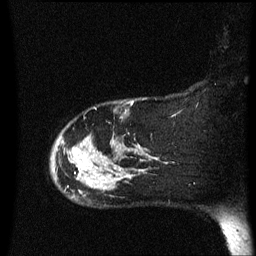
Breast MRI (dynamic contrast-enhanced), one sagittal slice. Dynamic contrast-enhanced series, image 2 of 3 at this slice position (ordered by acquisition). 1.5 T. TE 4.2 ms, TR 8.4 ms. 256 × 256 image matrix, field of view 200 × 200 mm. Female patient, age 47 years.
Structures marked on this image (semi-automatically segmented with operator editing):
- analysis volume of interest (the breast-tissue region the enhancement analysis was run in; not a lesion): bounding box <52,111,145,200> (left, top, right, bottom; pixels)
- tumour enhancement mask (voxels above the 70 % enhancement threshold inside the analysis volume of interest): <72,148,141,189>